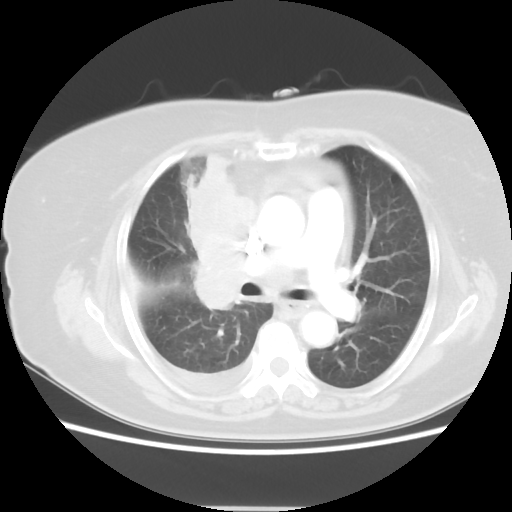
Chest CT, one axial slice. Slice 29 of 48 in the series (ordered by position). Reconstruction kernel STANDARD. 120 kVp. Lung window (W 1500 / L -600 HU). 5 mm slice thickness. 512 × 512 image matrix. Patient: female, 73 years. From the clinical record (not read from this slice): clinical TNM (as recorded): T3 N3 M1b.
Annotated regions visible in this slice (bounding box drawn by a radiologist):
- lung tumour (recorded histology: small cell carcinoma): bounding box (x1, y1, x2, y2) in pixels: (181, 150, 275, 326)